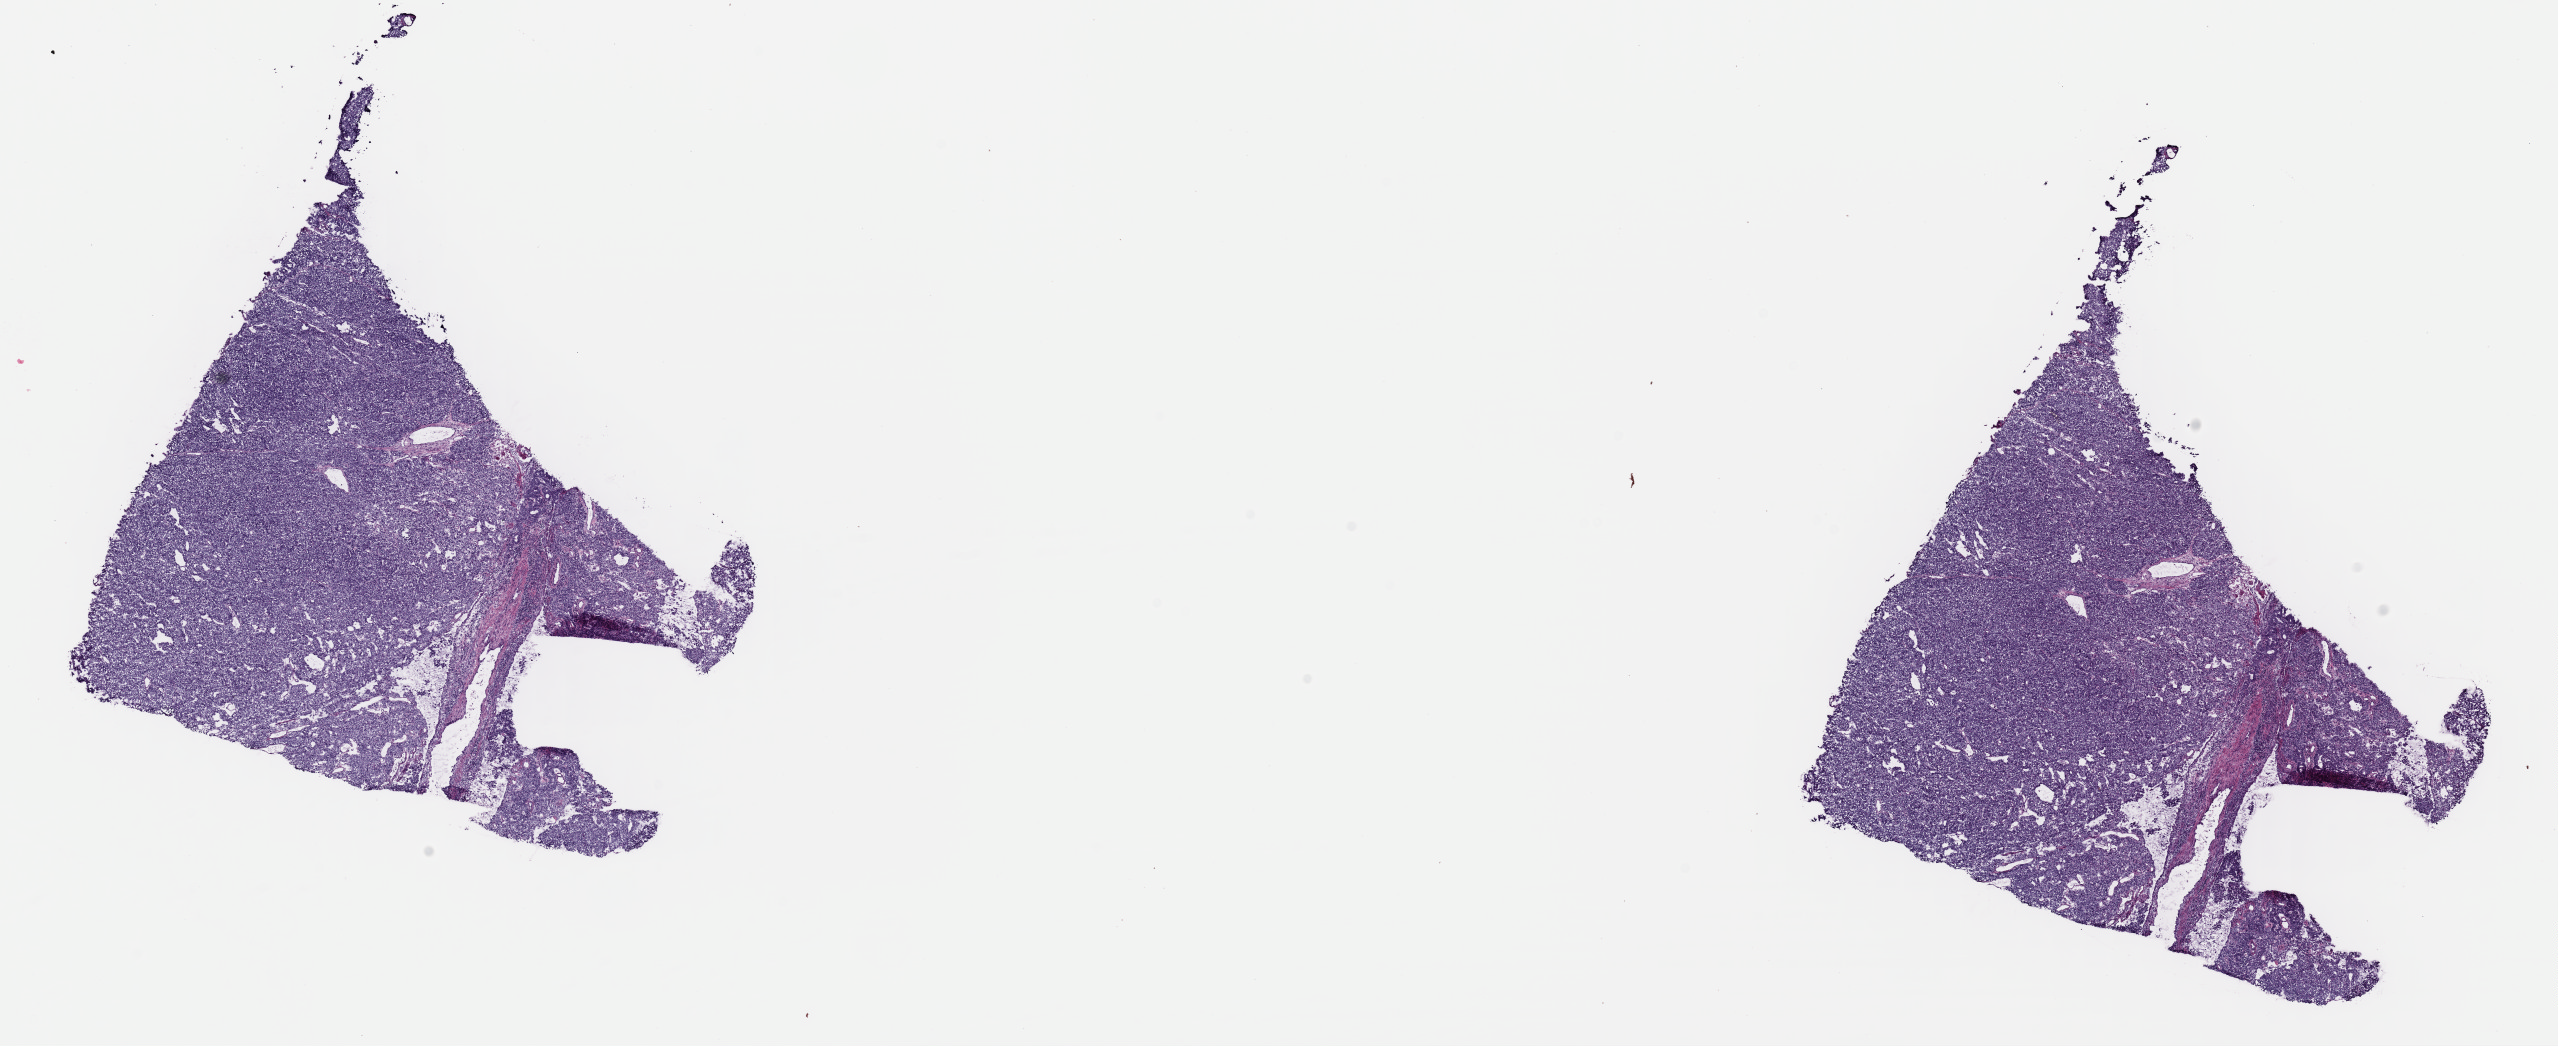
H&E whole-slide image, a low-resolution overview of the entire scanned area, about 20.2 x 8.3 mm; frozen section from the top of the tissue portion; primary tumour sample from the uterus. Female, age 50 years at initial diagnosis. Histologic grade: G3 (poorly differentiated). Pathologist review of this section (percent, as recorded): tumour cells 80%, tumour nuclei 90%, normal cells 10%, stromal cells 0%, necrosis 10%. Infiltration values recorded for this section: lymphocyte infiltration 10%, monocyte infiltration 0%, neutrophil infiltration 10%.
Diagnosis: Endometrioid adenocarcinoma, NOS. FIGO stage: IB. Lymph nodes positive (case pathology): 1 of 37 examined.